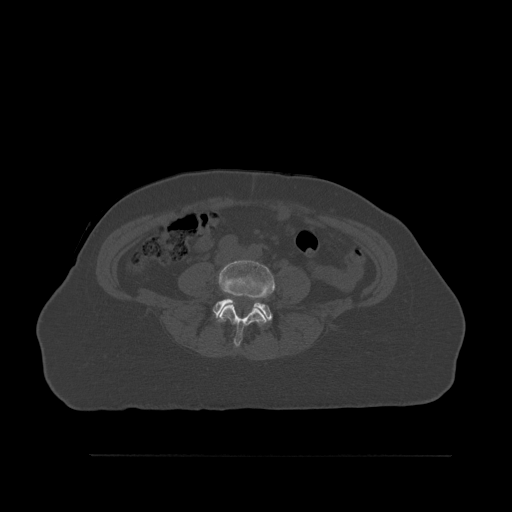
CT including the spine, one axial slice. Slice 200 of 527 in the series (ordered by position). Bone window (W 1800 / L 400 HU). 1.5 mm slice thickness. 512 × 512 image matrix, field of view 470 × 470 mm. Female patient, age 73 years. Case-level facts recorded for this patient, not image findings: primary cancer: breast; vertebrae with lytic lesions (as recorded): L2.
Annotated regions visible in this slice (semi-automatically segmented with operator editing):
- L4 vertebra: bounding box <218,260,275,348> (left, top, right, bottom; pixels)
- L5 vertebra: <213,299,273,325>